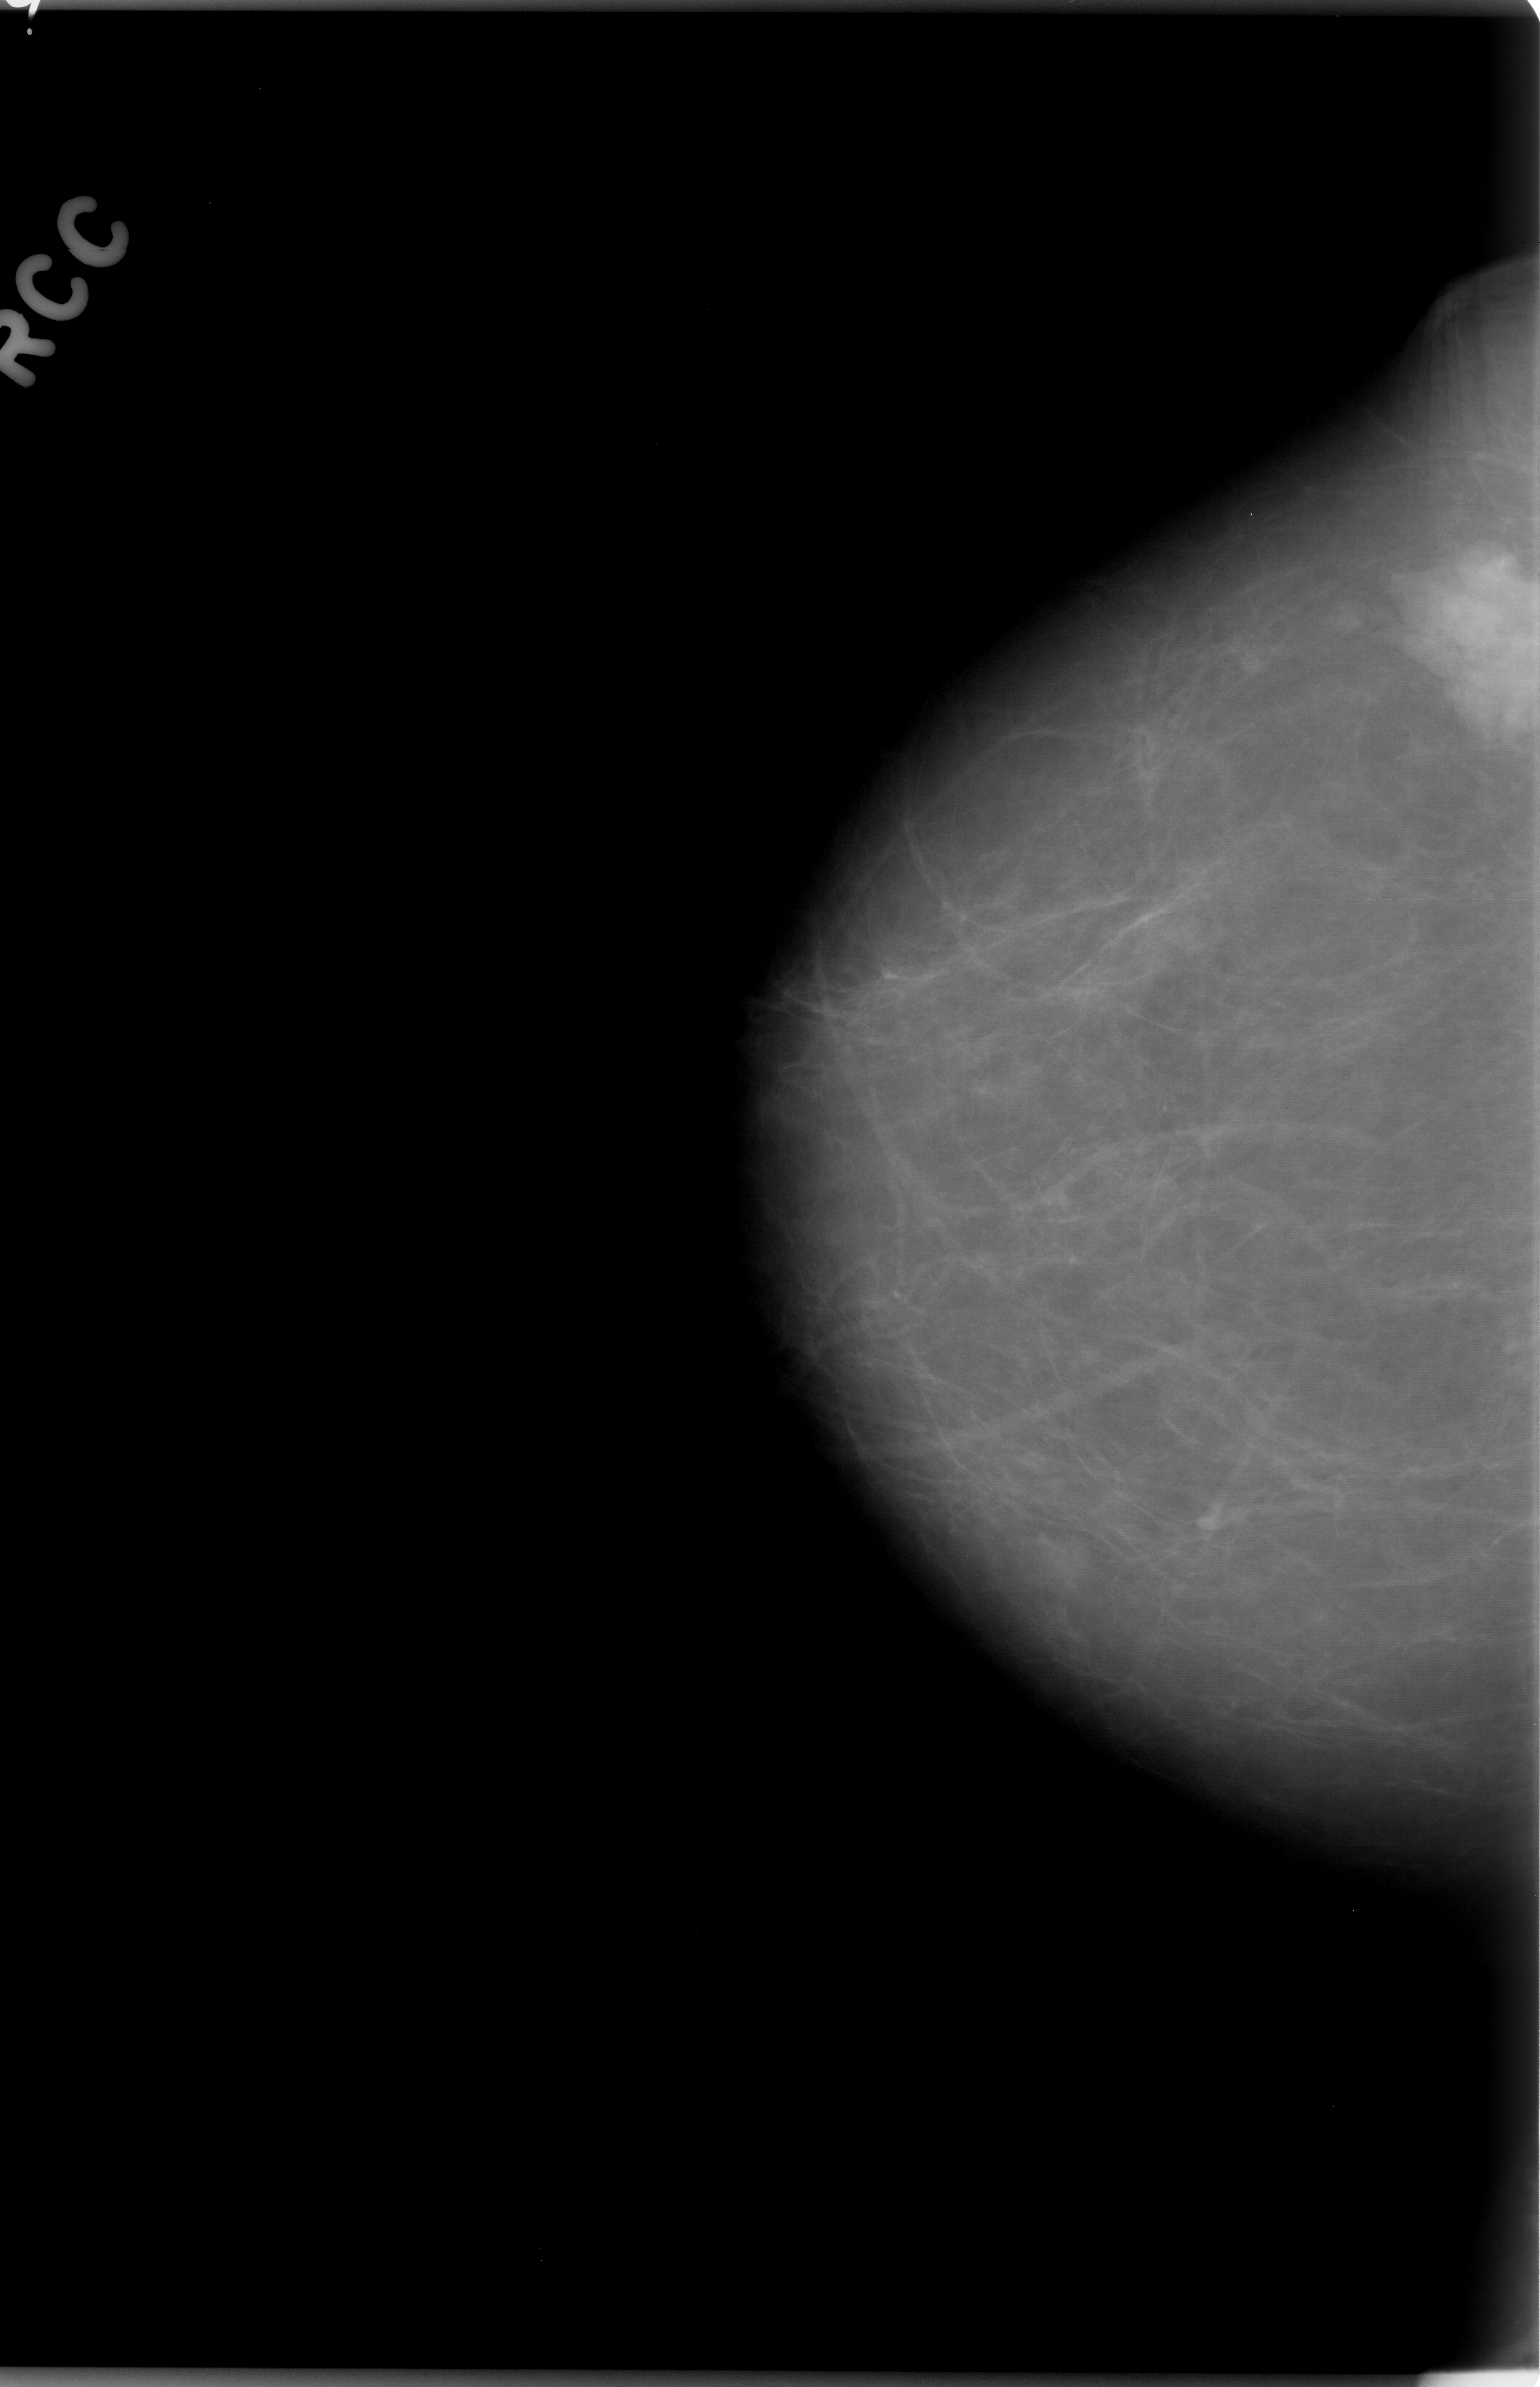
Scanned film-screen mammogram; right breast; craniocaudal (CC) view.
Radiologist-marked abnormalities on this image: mass, shape lobulated, margins microlobulated; BI-RADS assessment category 5; pathology (as recorded): malignant.